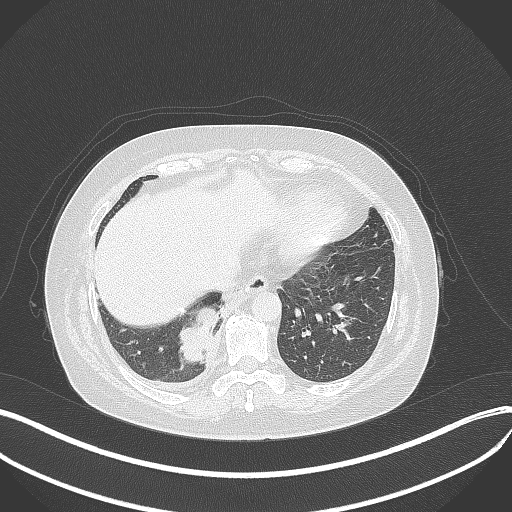
Chest CT, one axial slice. Slice 98 of 381 in the series (ordered by position). Lung window (W 1500 / L -600 HU). 1 mm slice thickness. 512 × 512 image matrix. Patient: female, 56 years. Case-level facts recorded for this patient, not image findings: clinical TNM (as recorded): T2b N1 M0; histopathological grade: G3.
Annotated regions visible in this slice (bounding box drawn by a radiologist):
- lung tumour (recorded histology: small cell carcinoma): bounding box [x1, y1, x2, y2] px = [169, 299, 219, 370]